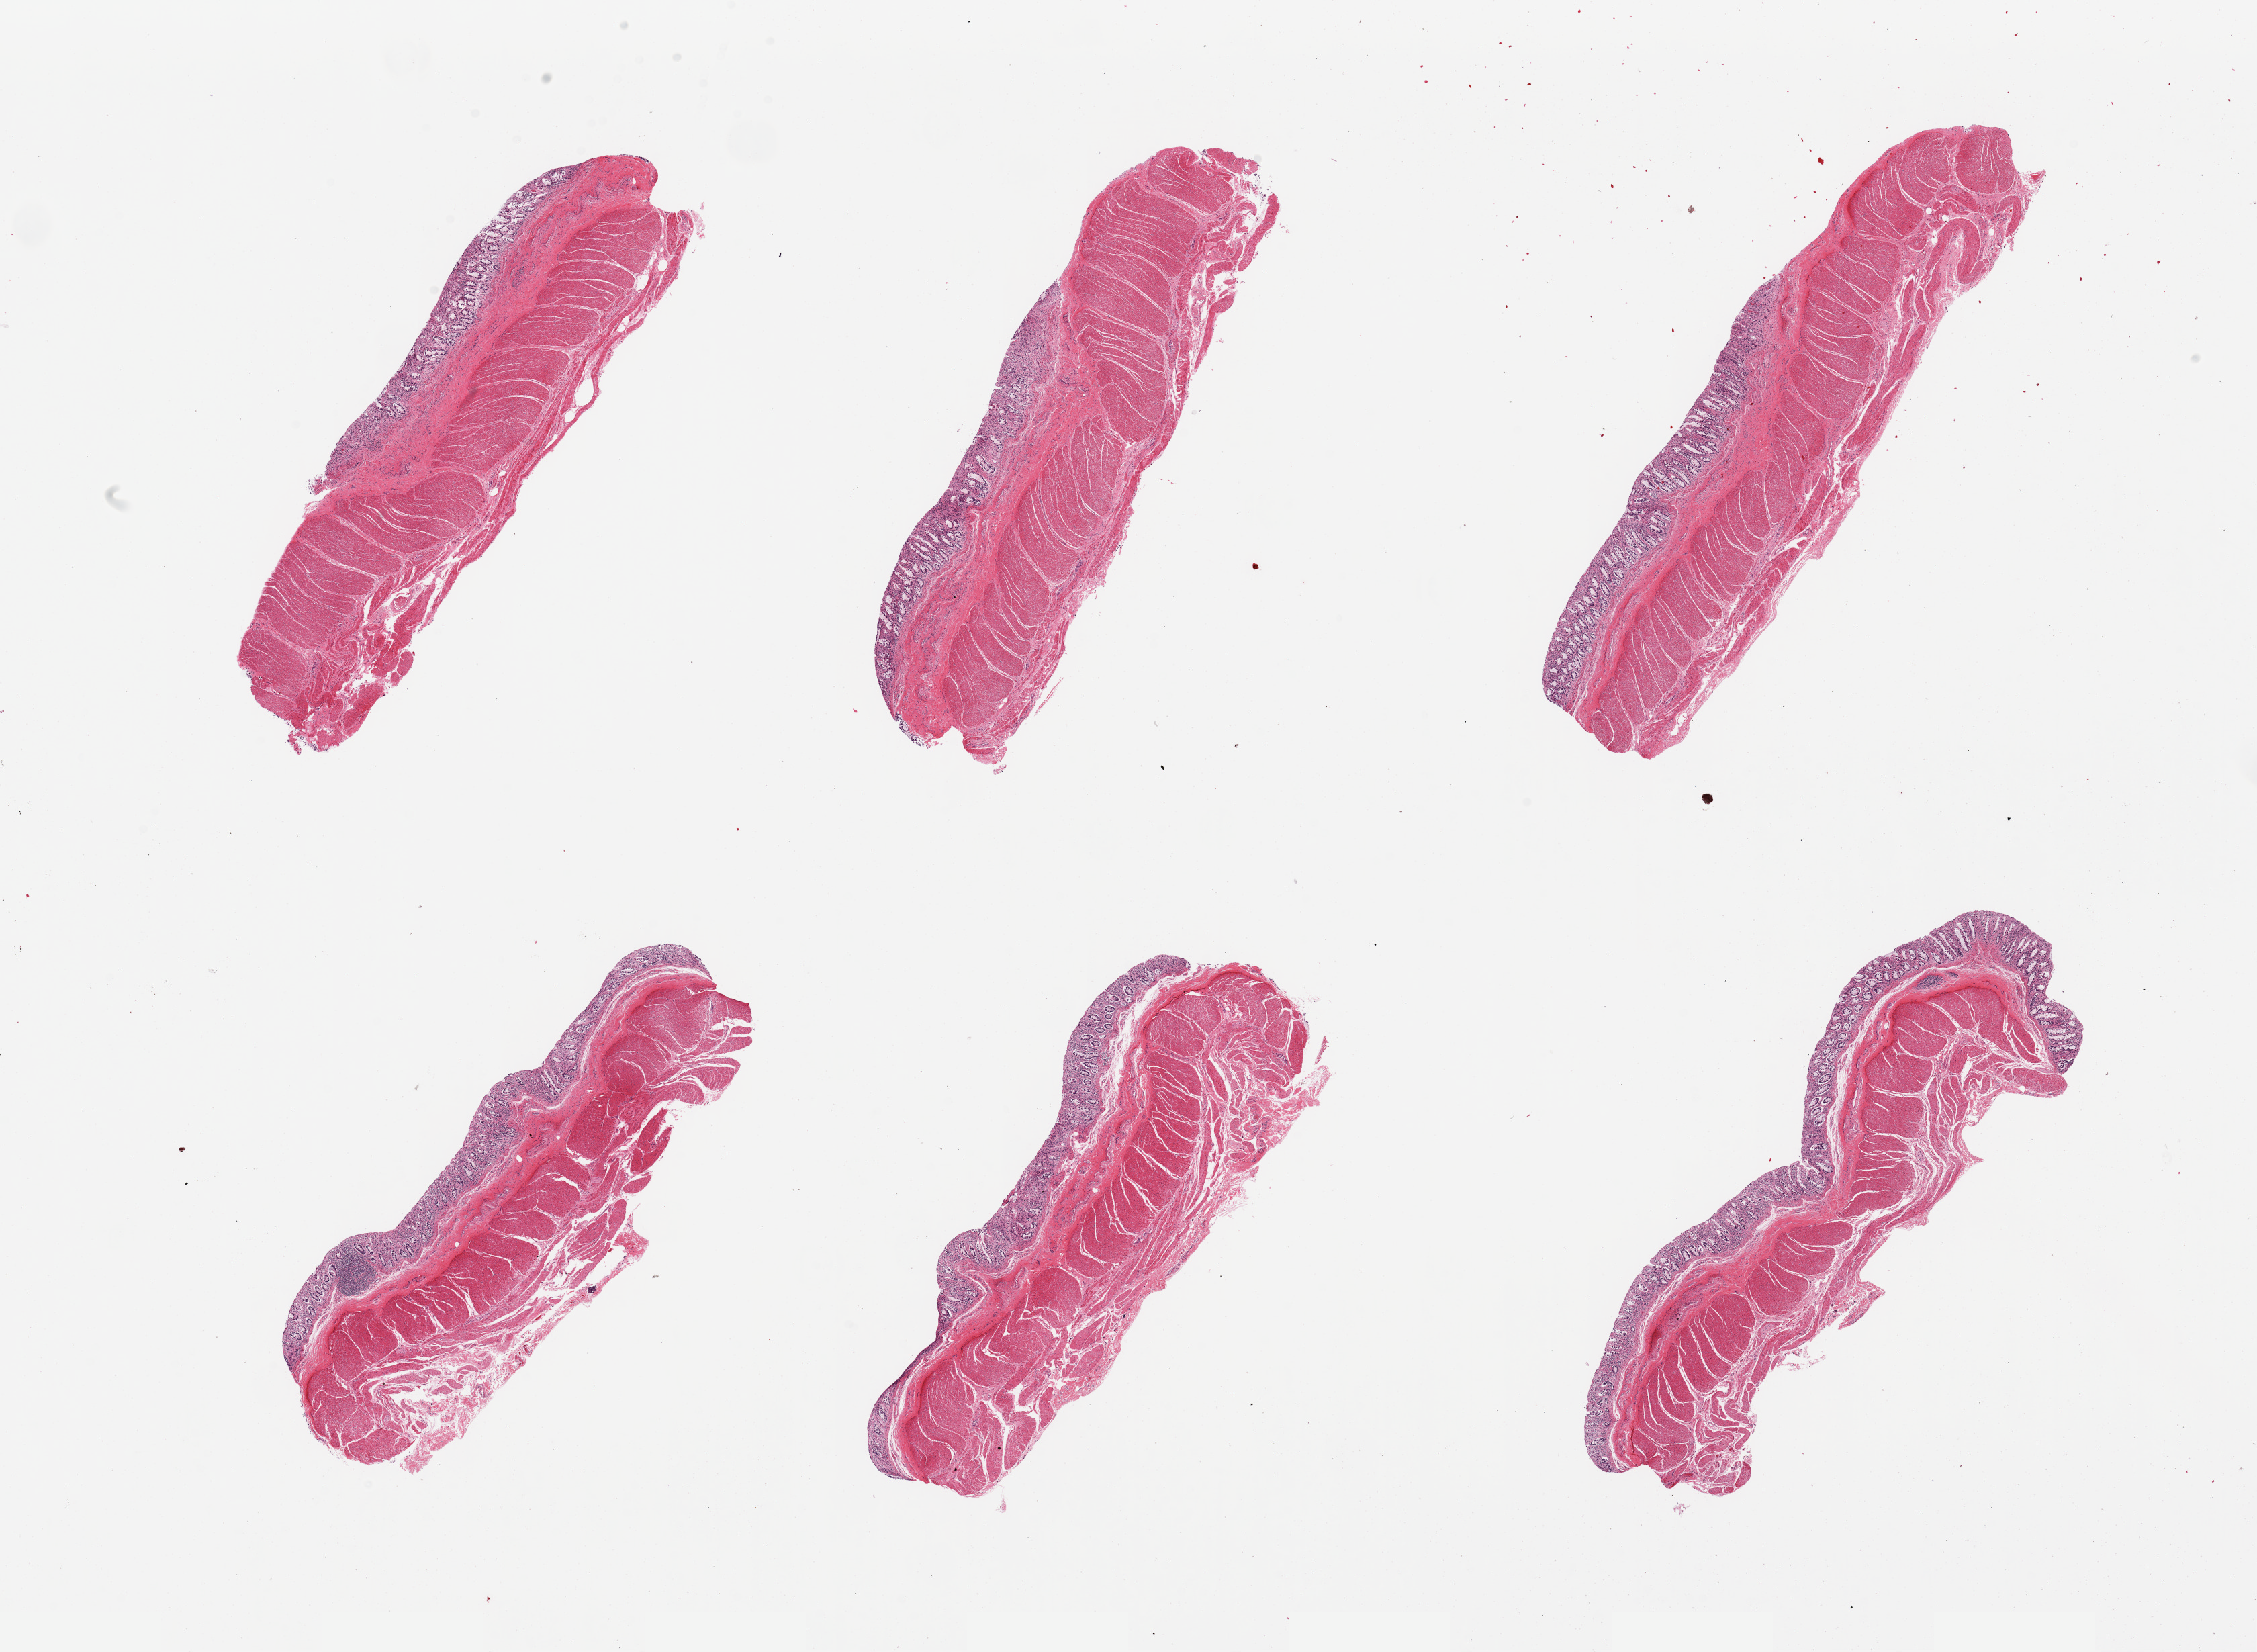
Digitized haematoxylin and eosin-stained section, a low-resolution overview of the entire scanned area, about 26.6 x 19.5 mm; PAXgene-fixed, paraffin-embedded tissue; target tissue: transverse colon; donor tissue sample. Donor: female.
Reviewer comment on this tissue sample: 6 pieces; mucosa badly autolyzed and/or sloughed, ~15-20% thickness.